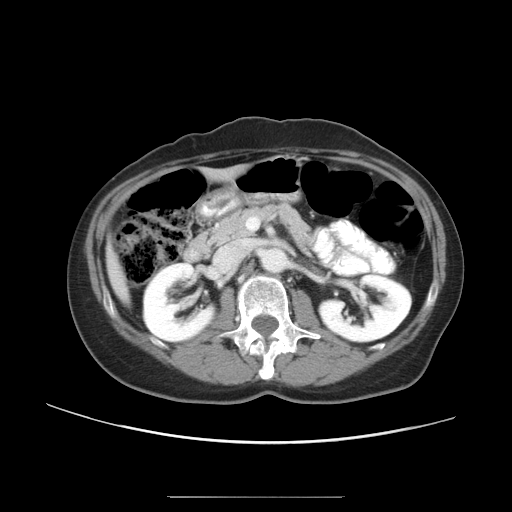
Contrast-enhanced abdominal CT, one axial slice; position 21 of 50 along the scan axis; 120 kVp; soft-tissue window (W 400 / L 40 HU); 5 mm slice thickness; 512 × 512 image matrix, field of view 389 × 389 mm. Female patient, age 58 years. Case-level facts recorded for this patient, not image findings: diagnosis: colorectal cancer liver metastases, imaged before liver resection; multiple liver metastases: yes; largest metastasis: 7.3 cm; chemotherapy before resection: yes.
Annotated regions visible in this slice (manually delineated by an expert):
- liver: bounding box (x1, y1, x2, y2) in pixels: (109, 256, 127, 297)